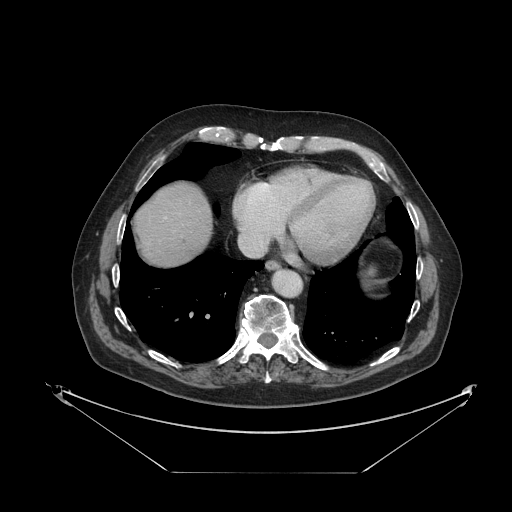
Contrast-enhanced abdominal CT, one axial slice; position 115 of 121 along the scan axis; reconstruction kernel STANDARD; 120 kVp; intravenous contrast given; soft-tissue window (W 400 / L 40 HU); 2.5 mm slice thickness; 512 × 512 image matrix, field of view 500 × 500 mm. Male patient, age 68 years. Case-level facts recorded for this patient, not image findings: diagnosis: colorectal cancer liver metastases, imaged before liver resection; multiple liver metastases: no; largest metastasis: 4 cm; disease in both lobes: no.
Outlined on this slice (expert manual segmentation):
- liver: bounding box <136,184,212,266> (left, top, right, bottom; pixels)
- planned liver remnant (the part of the liver to remain after resection): <136,184,212,266>